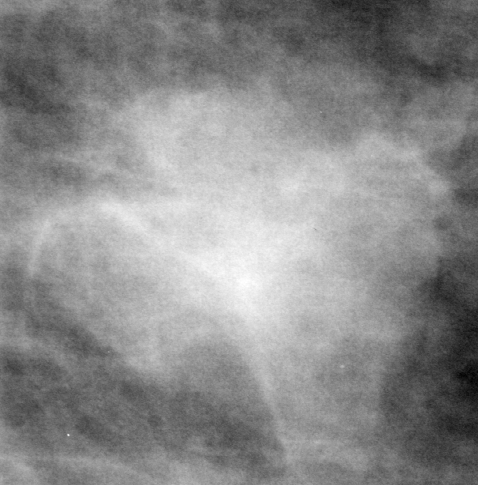
Cropped region of a digitized screen-film mammogram centred on a radiologist-marked abnormality; left breast; MLO view; BI-RADS breast density category 2 (scale 1–4).
- Finding: mass, shape lobulated, margins ill defined; BI-RADS assessment category 4; subtlety rating 4 on a 1 (subtle) to 5 (obvious) scale; pathology (as recorded): malignant.